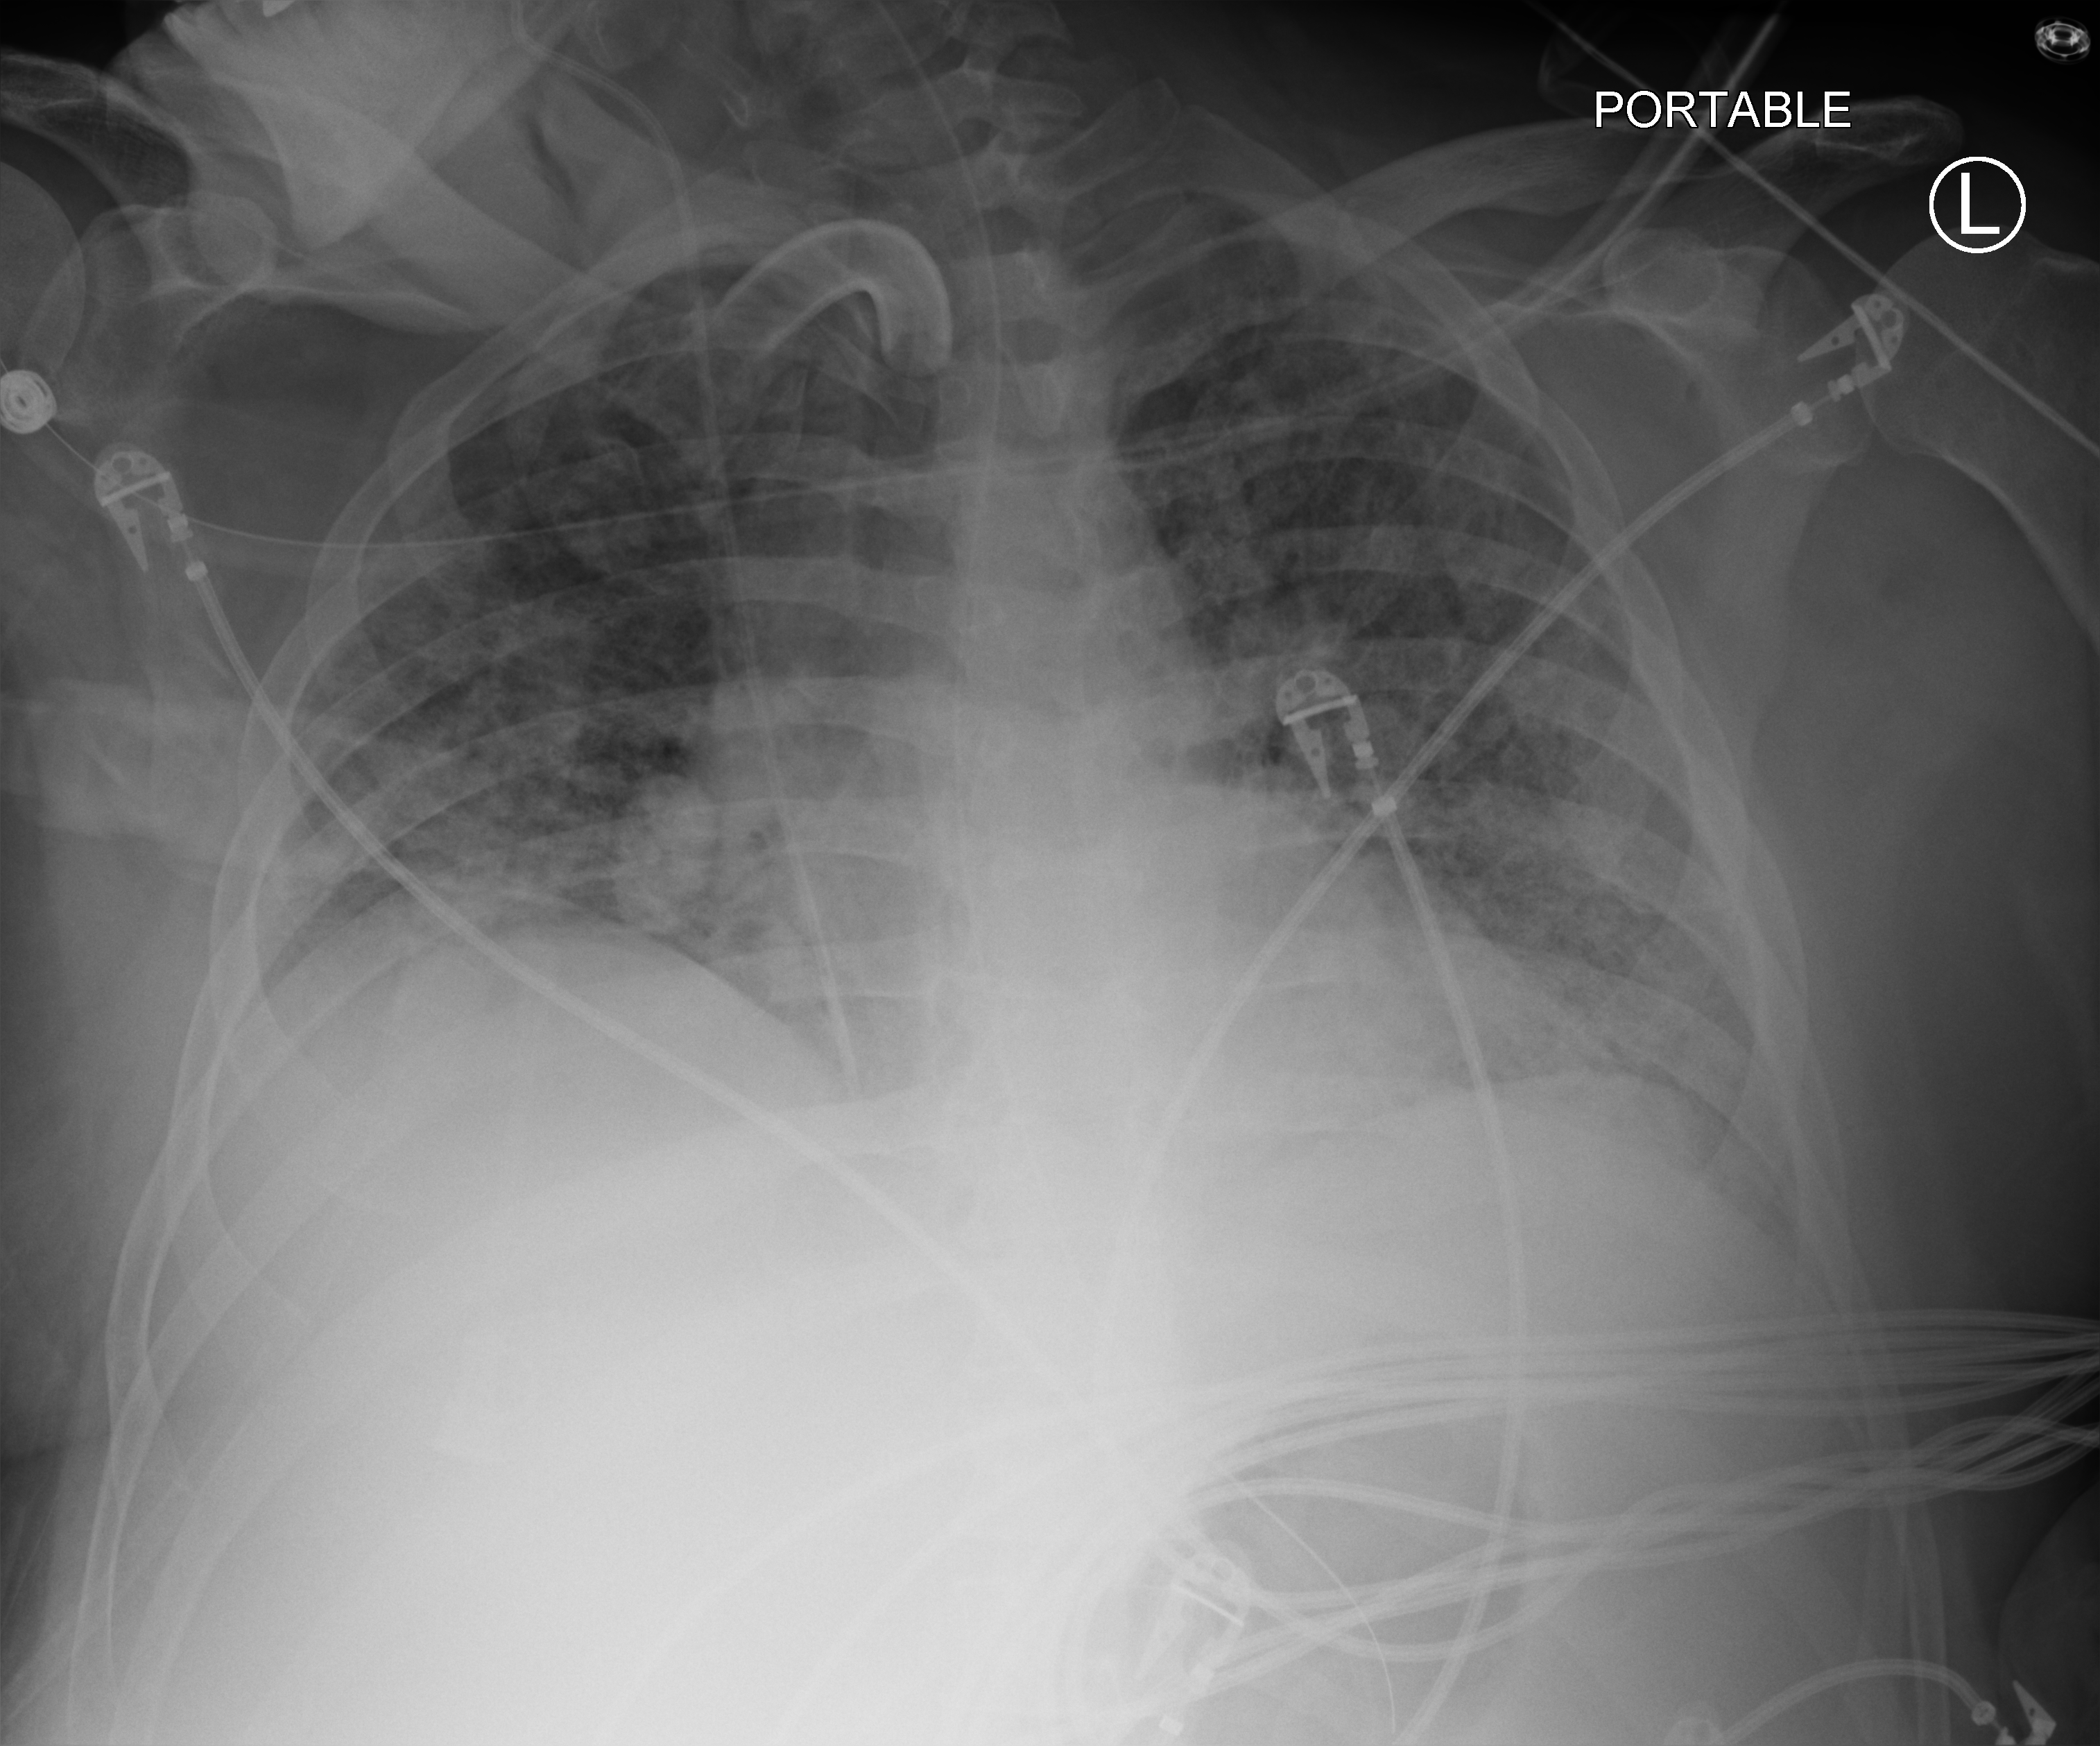
Portable chest radiograph; anteroposterior (AP) projection. Patient hospitalised with COVID-19; male, aged 18–59 years.
From the hospital-stay record, not from the radiograph (when in the stay this image was taken is not recorded): mechanically ventilated during this hospital stay: yes; hypertension (admission record): yes; diabetes (admission record): no.